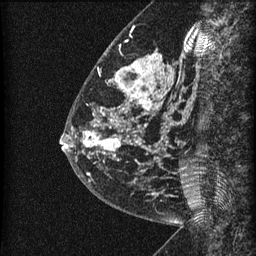
Breast MRI (dynamic contrast-enhanced), one sagittal slice; position 20 of 60 along the scan axis; dynamic contrast-enhanced series, image 2 of 3 at this slice position (ordered by acquisition); 1.5 T; TE 4.2 ms, TR 22.7 ms; 256 × 256 image matrix, field of view 180 × 180 mm. Female patient, age 48 years. From the clinical record (not read from this slice): setting: breast cancer imaged before/during neoadjuvant chemotherapy; receptor status: triple-negative.
Annotated regions visible in this slice (semi-automatically segmented with operator editing):
- analysis volume of interest (the breast-tissue region the enhancement analysis was run in; not a lesion): bounding box (x1, y1, x2, y2) in pixels: (81, 23, 186, 202)
- tumour enhancement mask (voxels above the 90 % enhancement threshold inside the analysis volume of interest): (82, 55, 167, 195)